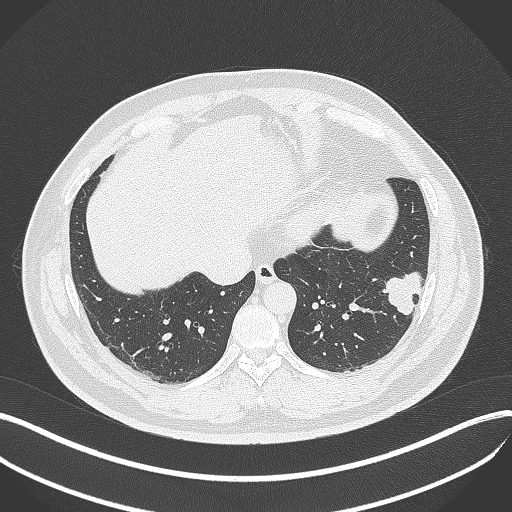
Chest CT, one axial slice. Position 124 of 429 along the scan axis. 120 kVp. Lung window (W 1500 / L -600 HU). 512 × 512 image matrix, field of view 400 × 400 mm. Male patient, age 39 years. From the clinical record (not read from this slice): clinical TNM (as recorded): T2a N0 M0; histopathological grade: G2-3.
Structures marked on this image (bounding box drawn by a radiologist):
- lung tumour (recorded histology: adenocarcinoma): bounding box [x1, y1, x2, y2] px = [376, 271, 425, 318]